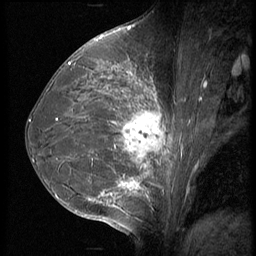
Breast MRI (dynamic contrast-enhanced), one sagittal slice. Slice 30 of 56 in the series (ordered by position). 3 images stored at this slice position (order not interpretable as contrast timing). 1.5 T. TE 4.2 ms, TR 9 ms. 2.5 mm slice thickness. 256 × 256 image matrix, field of view 180 × 180 mm. Female patient, age 35 years. From the clinical record (not read from this slice): setting: breast cancer imaged before/during neoadjuvant chemotherapy; receptor status: HR-positive, HER2-negative.
Structures marked on this image (semi-automatic segmentation, software-assisted and operator-edited):
- analysis volume of interest (the breast-tissue region the enhancement analysis was run in; not a lesion): bounding box [x1, y1, x2, y2] px = [63, 60, 190, 218]
- tumour enhancement mask (voxels above the 140 % enhancement threshold inside the analysis volume of interest): [69, 63, 166, 198]